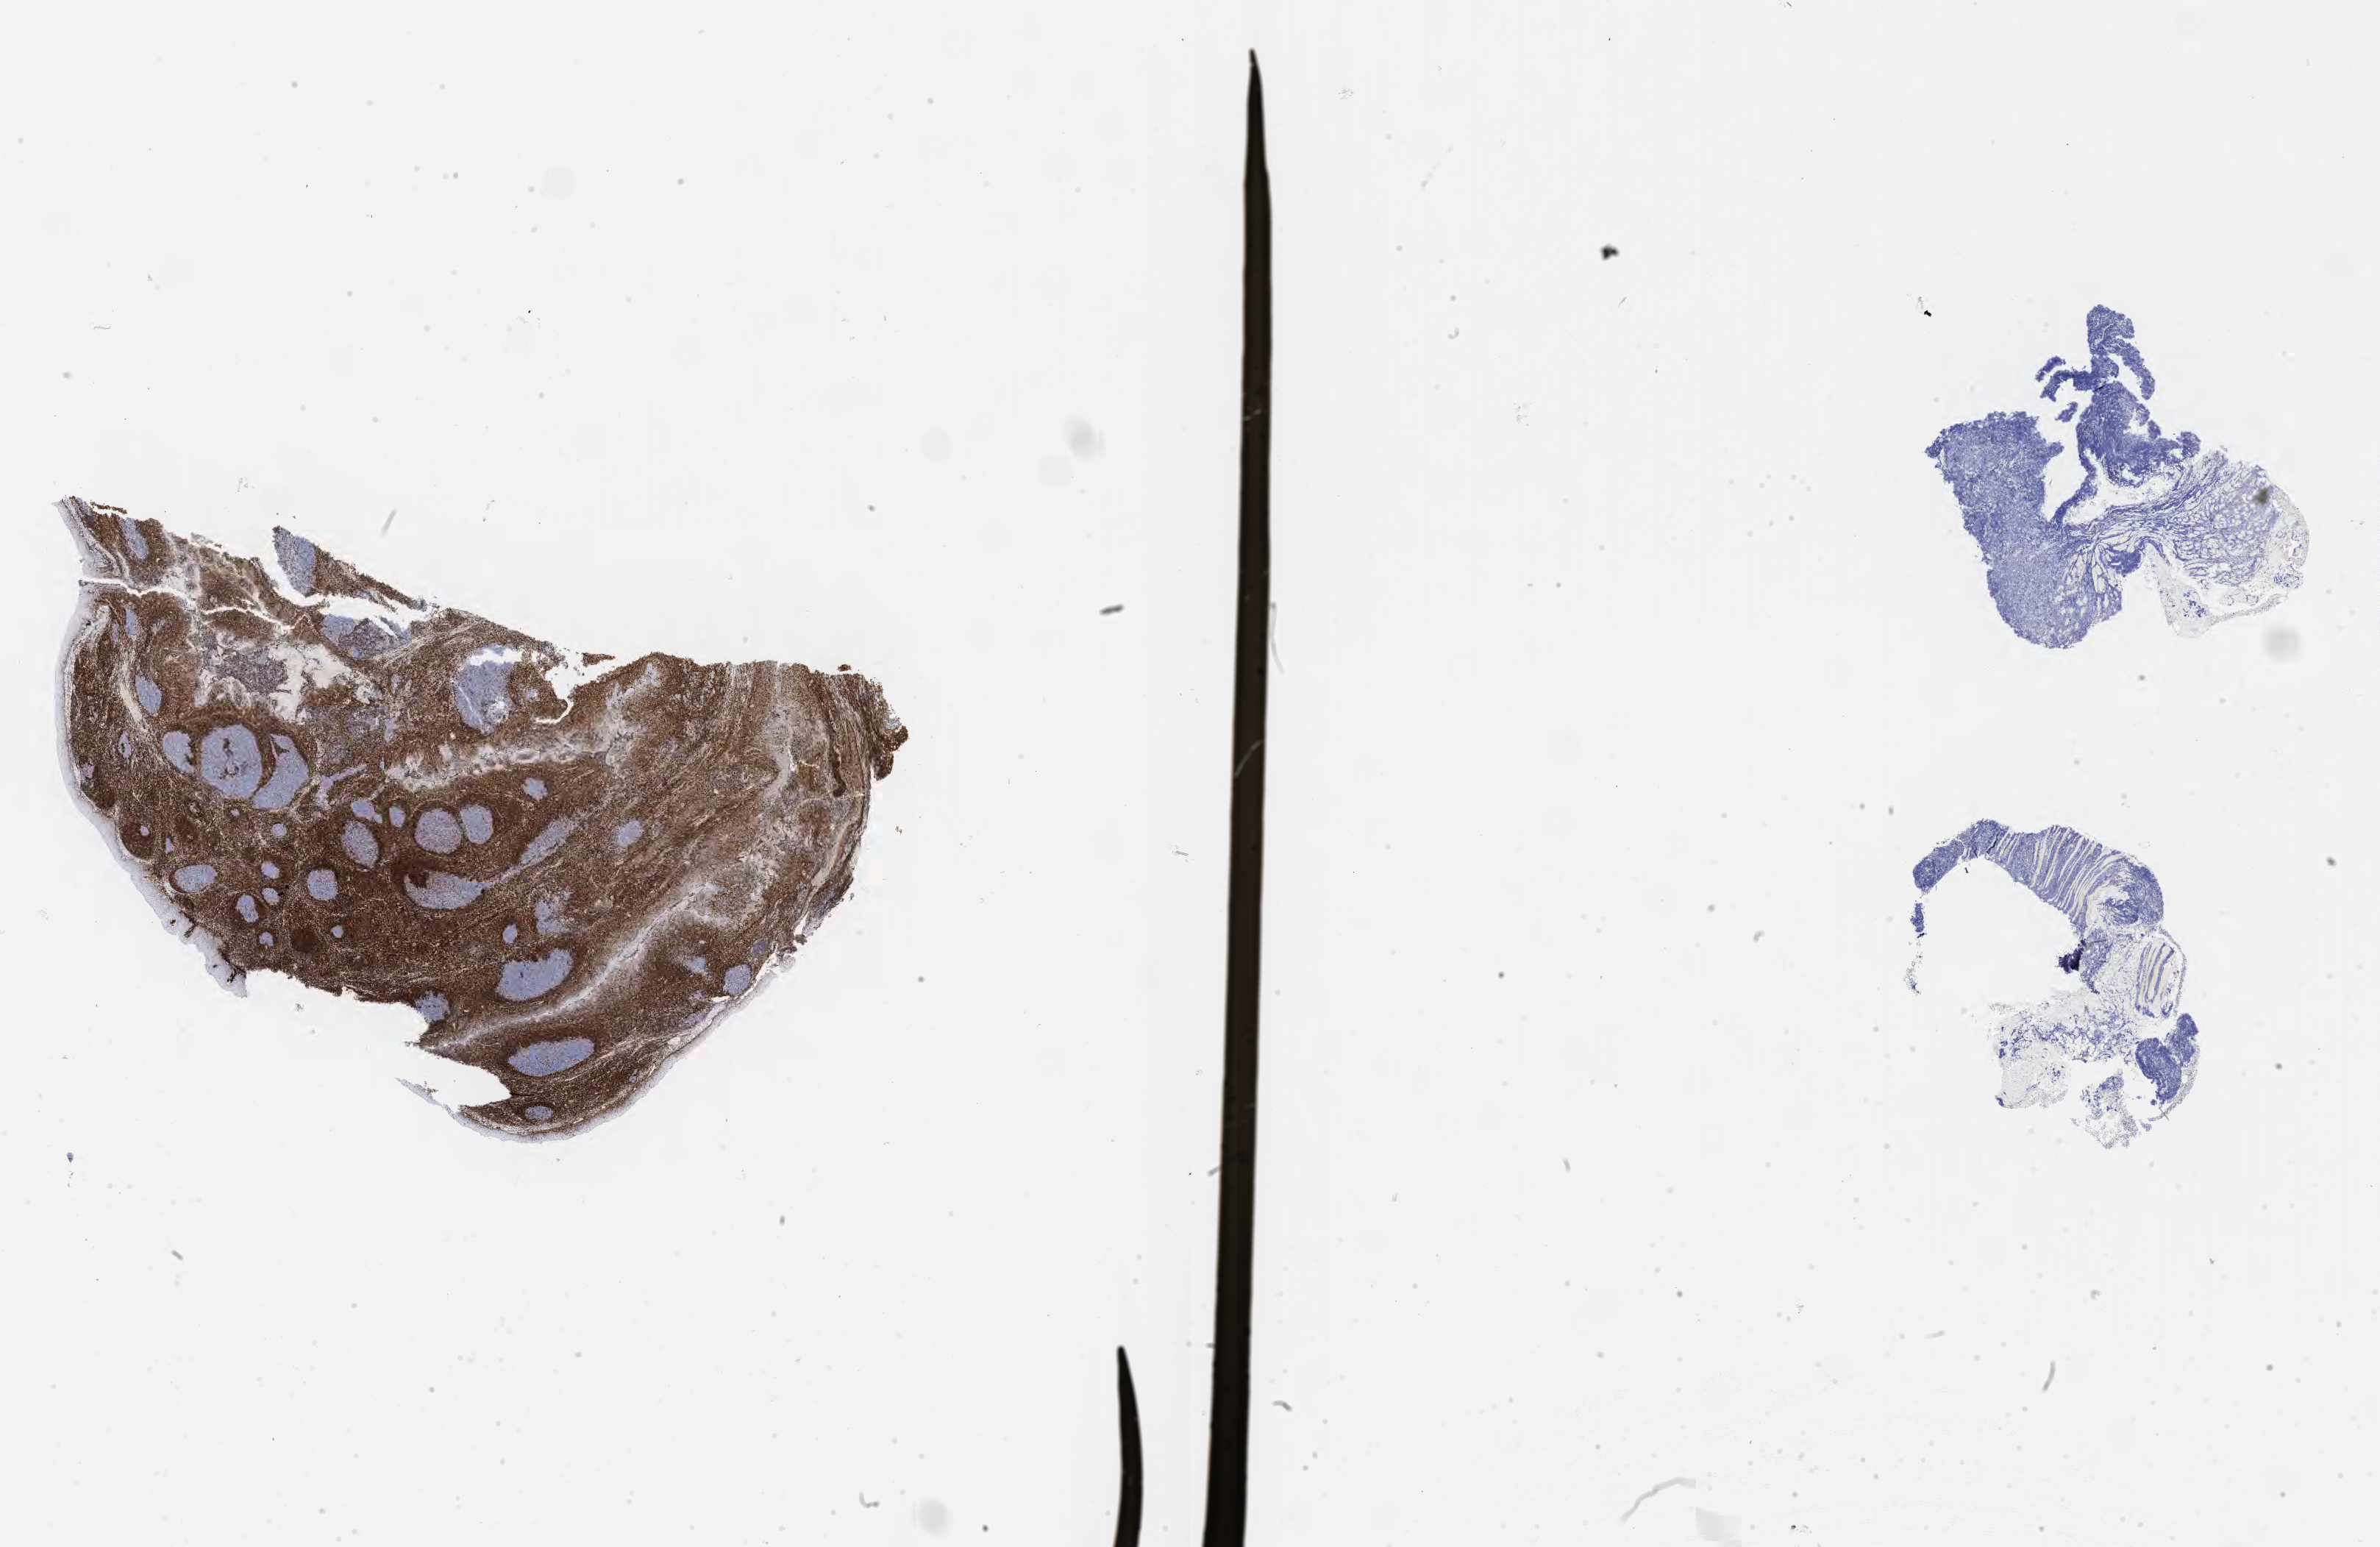
Whole-slide image, immunohistochemical stain for BCL2 — whole scanned area (about 26.2 x 17.0 mm) shown as a low-resolution overview; specimen: tumor tissue; anatomic site: lymph node of head and neck. Patient male; aged 73.
Histologic diagnosis: Burkitt lymphoma, NOS.